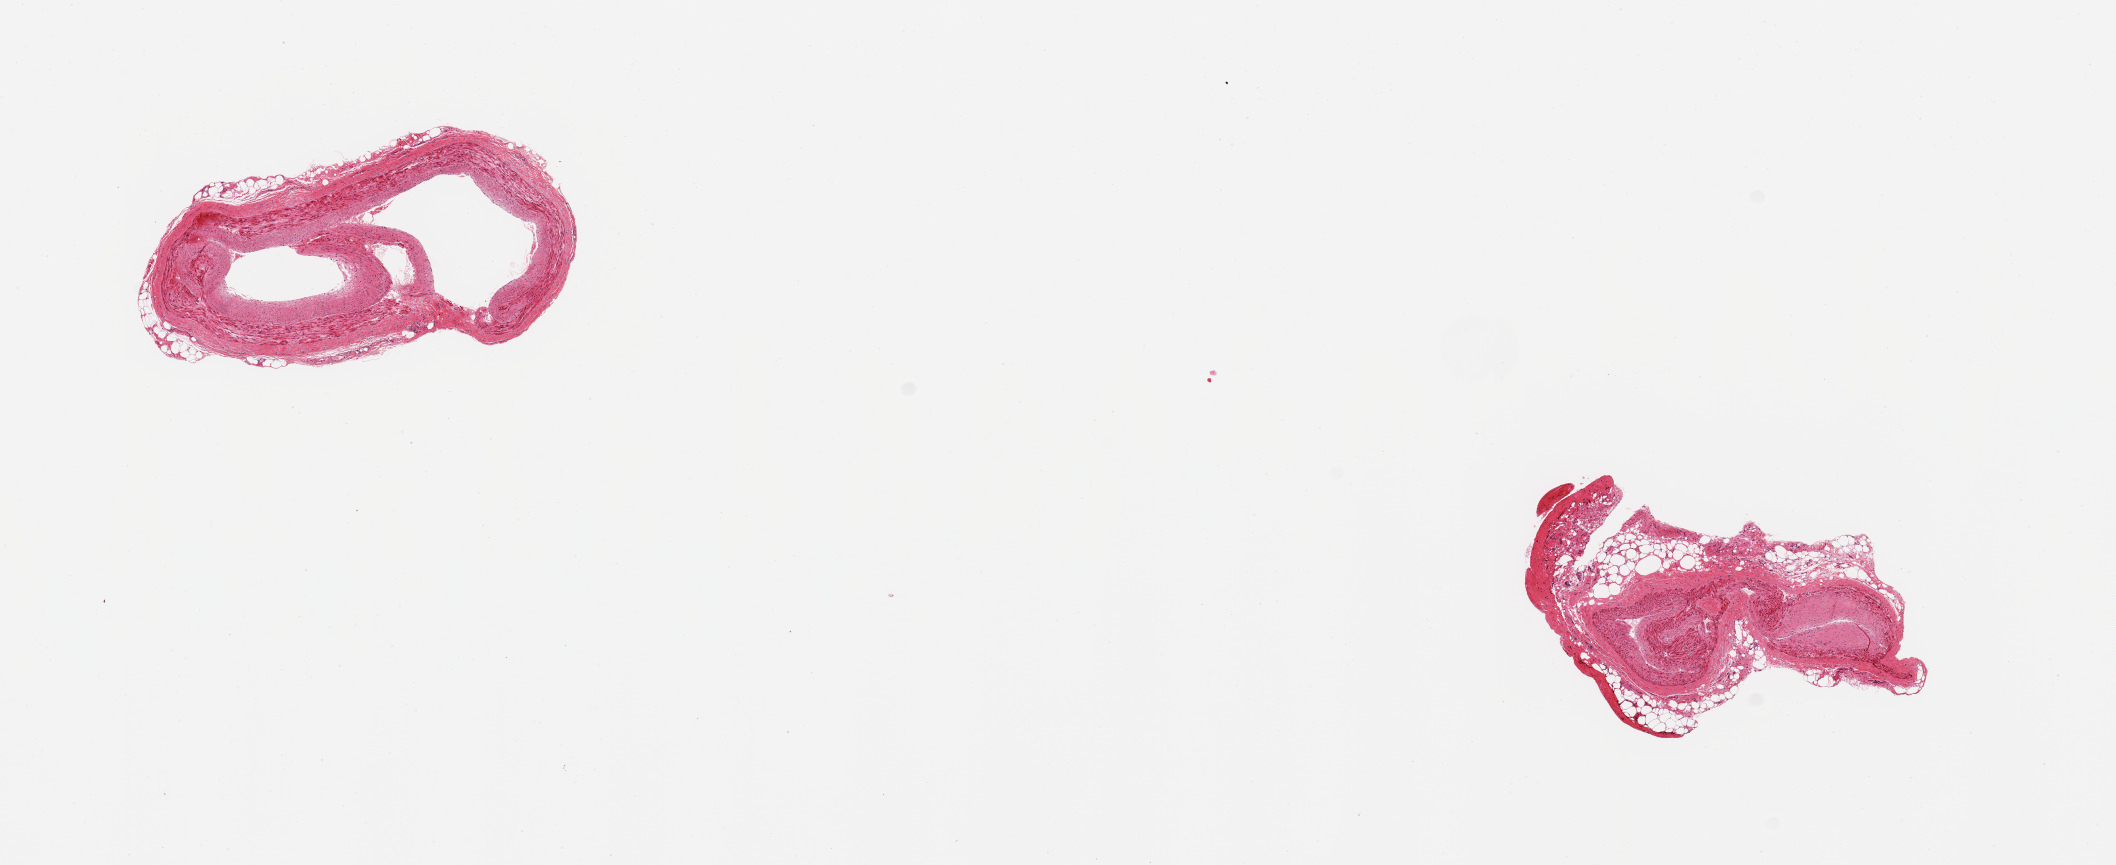
Digitized H&E-stained section, a low-resolution overview of the entire scanned area, about 16.7 x 6.8 mm; PAXgene-fixed paraffin-embedded (PFPE) section; target tissue: coronary artery; donor tissue sample. Donor: male.
Pathologist's review note for this sample: 2 pieces; one with collapsed lumen, eccentric early atherosclerotic change and 30% external fat.